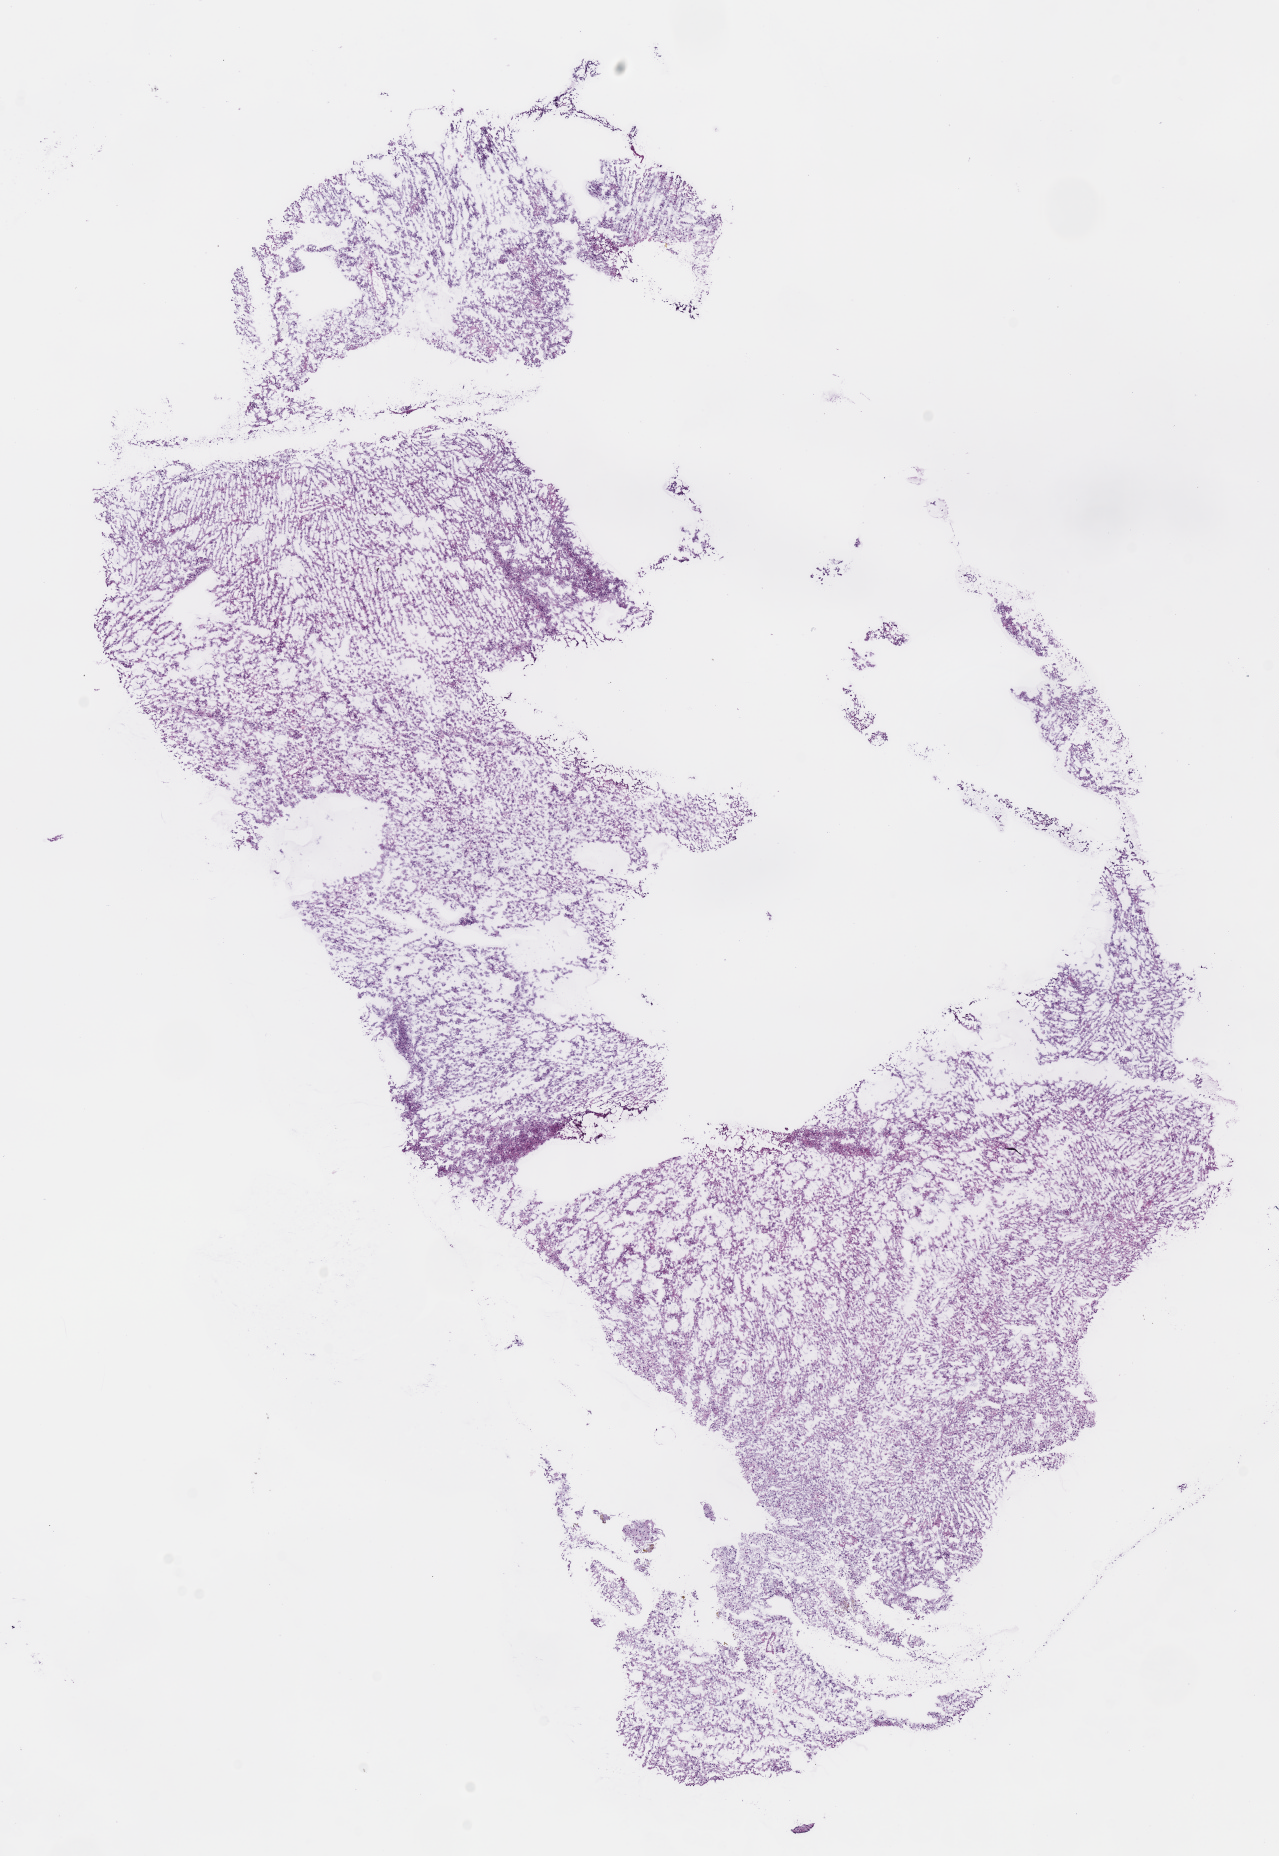
Whole-slide histology image, H&E, whole scanned area (about 10.1 x 14.6 mm, acquisition: 40x scan) shown as a low-resolution overview, frozen section, sample: primary tumour, brain. Patient: male, age at initial diagnosis 50 years. Histologic grade: G2 (moderately differentiated). Pathologist review of this section (percent, as recorded): tumour cells 100%, tumour nuclei 75%, normal cells 0%, stromal cells 0%, necrosis 0%.
Histologic diagnosis: Astrocytoma, NOS (cerebrum). Laterality: left.